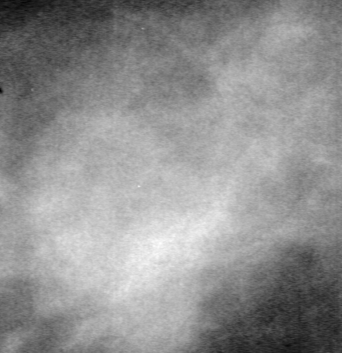
Cropped region of a digitized screen-film mammogram centred on a radiologist-marked abnormality; left breast; MLO view; BI-RADS breast density category 1 (scale 1–4).
Finding: mass, shape lobulated, margins obscured; BI-RADS assessment category 3; subtlety rating 3 on a 1 (subtle) to 5 (obvious) scale; pathology (as recorded): benign.